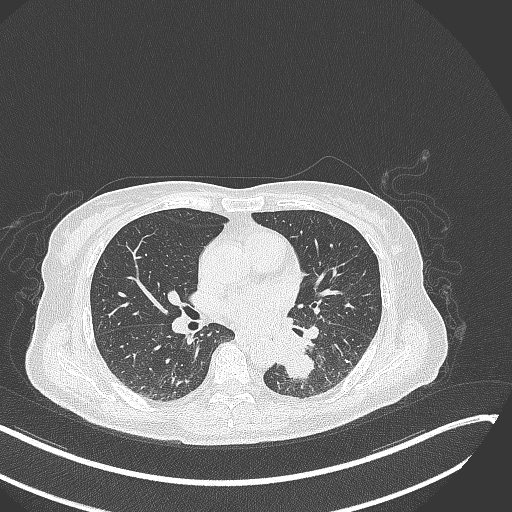
Chest CT, one axial slice. Slice 135 of 342 in the series (ordered by position). Reconstruction kernel B70f. Lung window (W 1500 / L -600 HU). 1 mm slice thickness. 512 × 512 image matrix. Patient: female, 64 years. Case-level facts recorded for this patient, not image findings: clinical TNM (as recorded): T3 N1 M1; histopathological grade: G3.
Annotated regions visible in this slice (rectangle marked by the reading radiologist):
- lung tumour (recorded histology: small cell carcinoma): bounding box (x1, y1, x2, y2) in pixels: (267, 328, 324, 388)